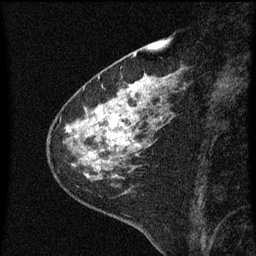
Breast MRI (dynamic contrast-enhanced), one sagittal slice; position 18 of 60 along the scan axis; dynamic contrast-enhanced series, image 2 of 3 at this slice position (ordered by acquisition); 1.5 T; TE 4.2 ms, TR 8 ms; 2 mm slice thickness; 256 × 256 image matrix, field of view 180 × 180 mm. Female patient, age 60 years.
Outlined on this slice (semi-automatically segmented with operator editing):
- analysis volume of interest (the breast-tissue region the enhancement analysis was run in; not a lesion): bounding box [x1, y1, x2, y2] px = [49, 82, 159, 181]
- tumour enhancement mask (voxels above the 70 % enhancement threshold inside the analysis volume of interest): [67, 84, 141, 171]